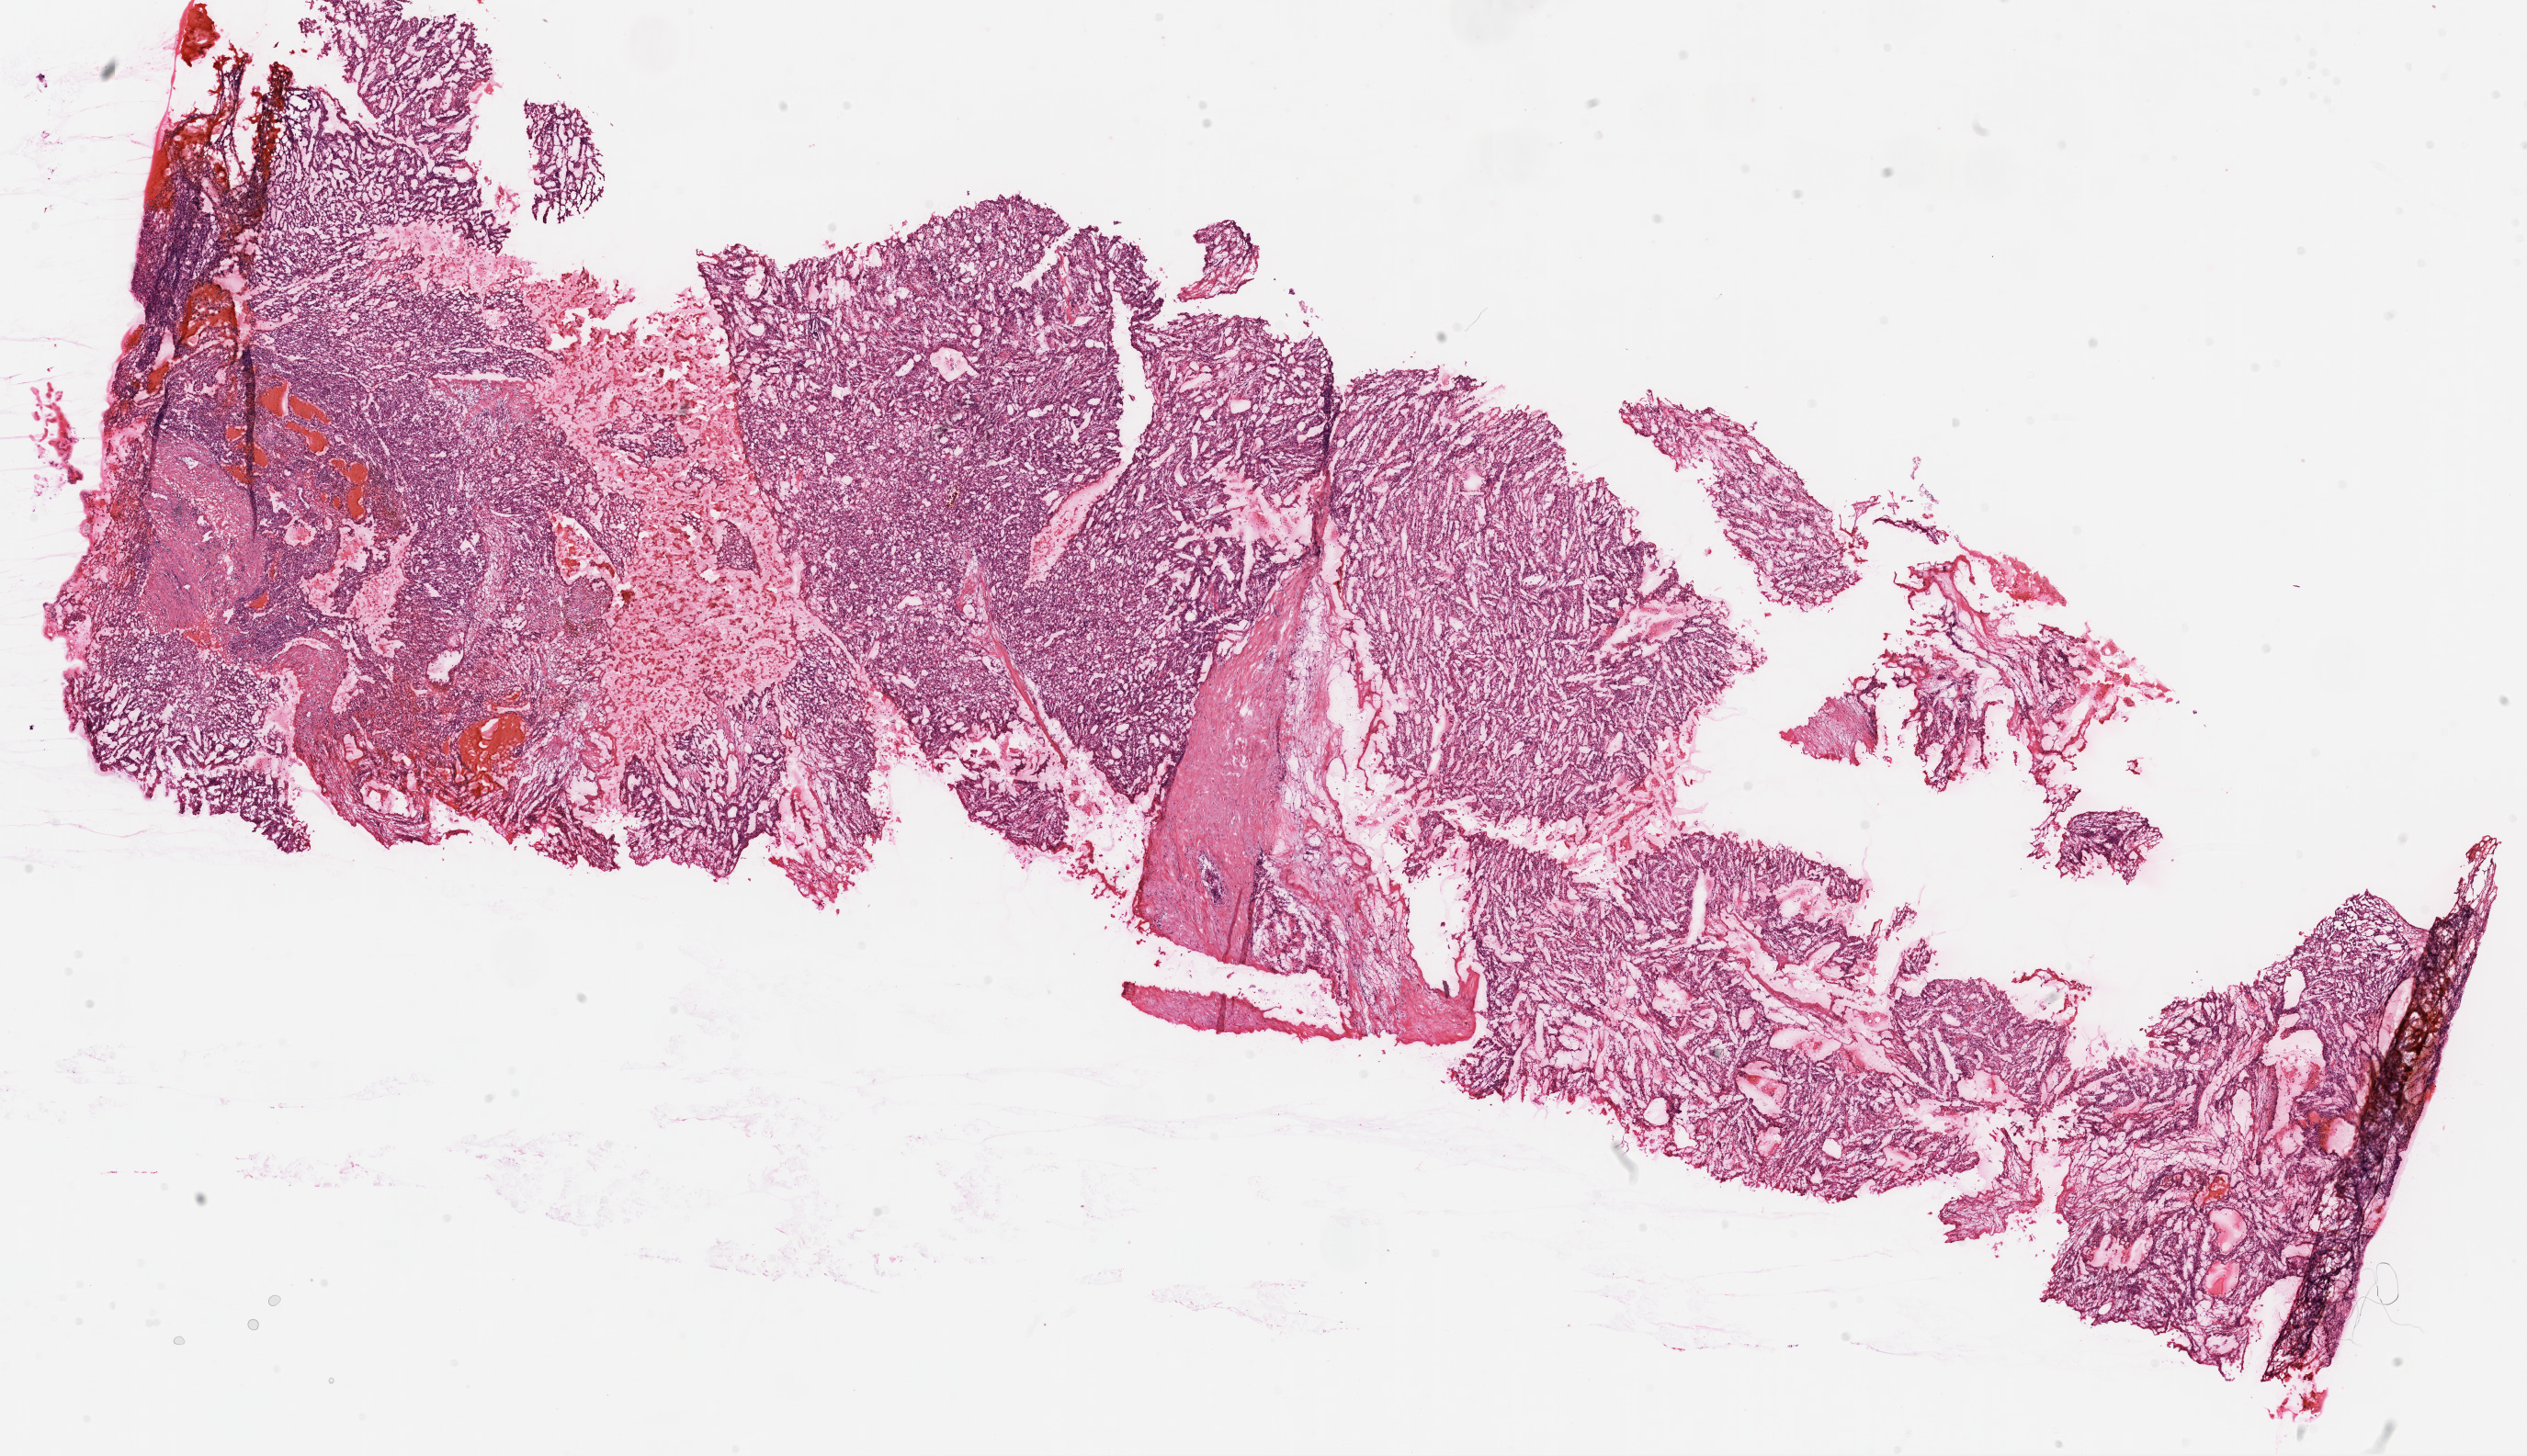
Digitized H&E tissue section (whole slide), shown as a low-resolution overview of the whole scanned area (about 22.1 x 12.7 mm, acquisition: 20x scan), frozen section from the top of the tissue portion, kidney, primary tumour sample. Patient: male, age at initial diagnosis 49 years. Histologic grade: G4 (undifferentiated). Slide review estimates, as recorded: tumour cells 80%, tumour nuclei 80%, normal cells 0%, stromal cells 20%, necrosis 0%.
• laterality: left
• AJCC pathologic stage: III
• pathologic diagnosis: Clear cell adenocarcinoma, NOS